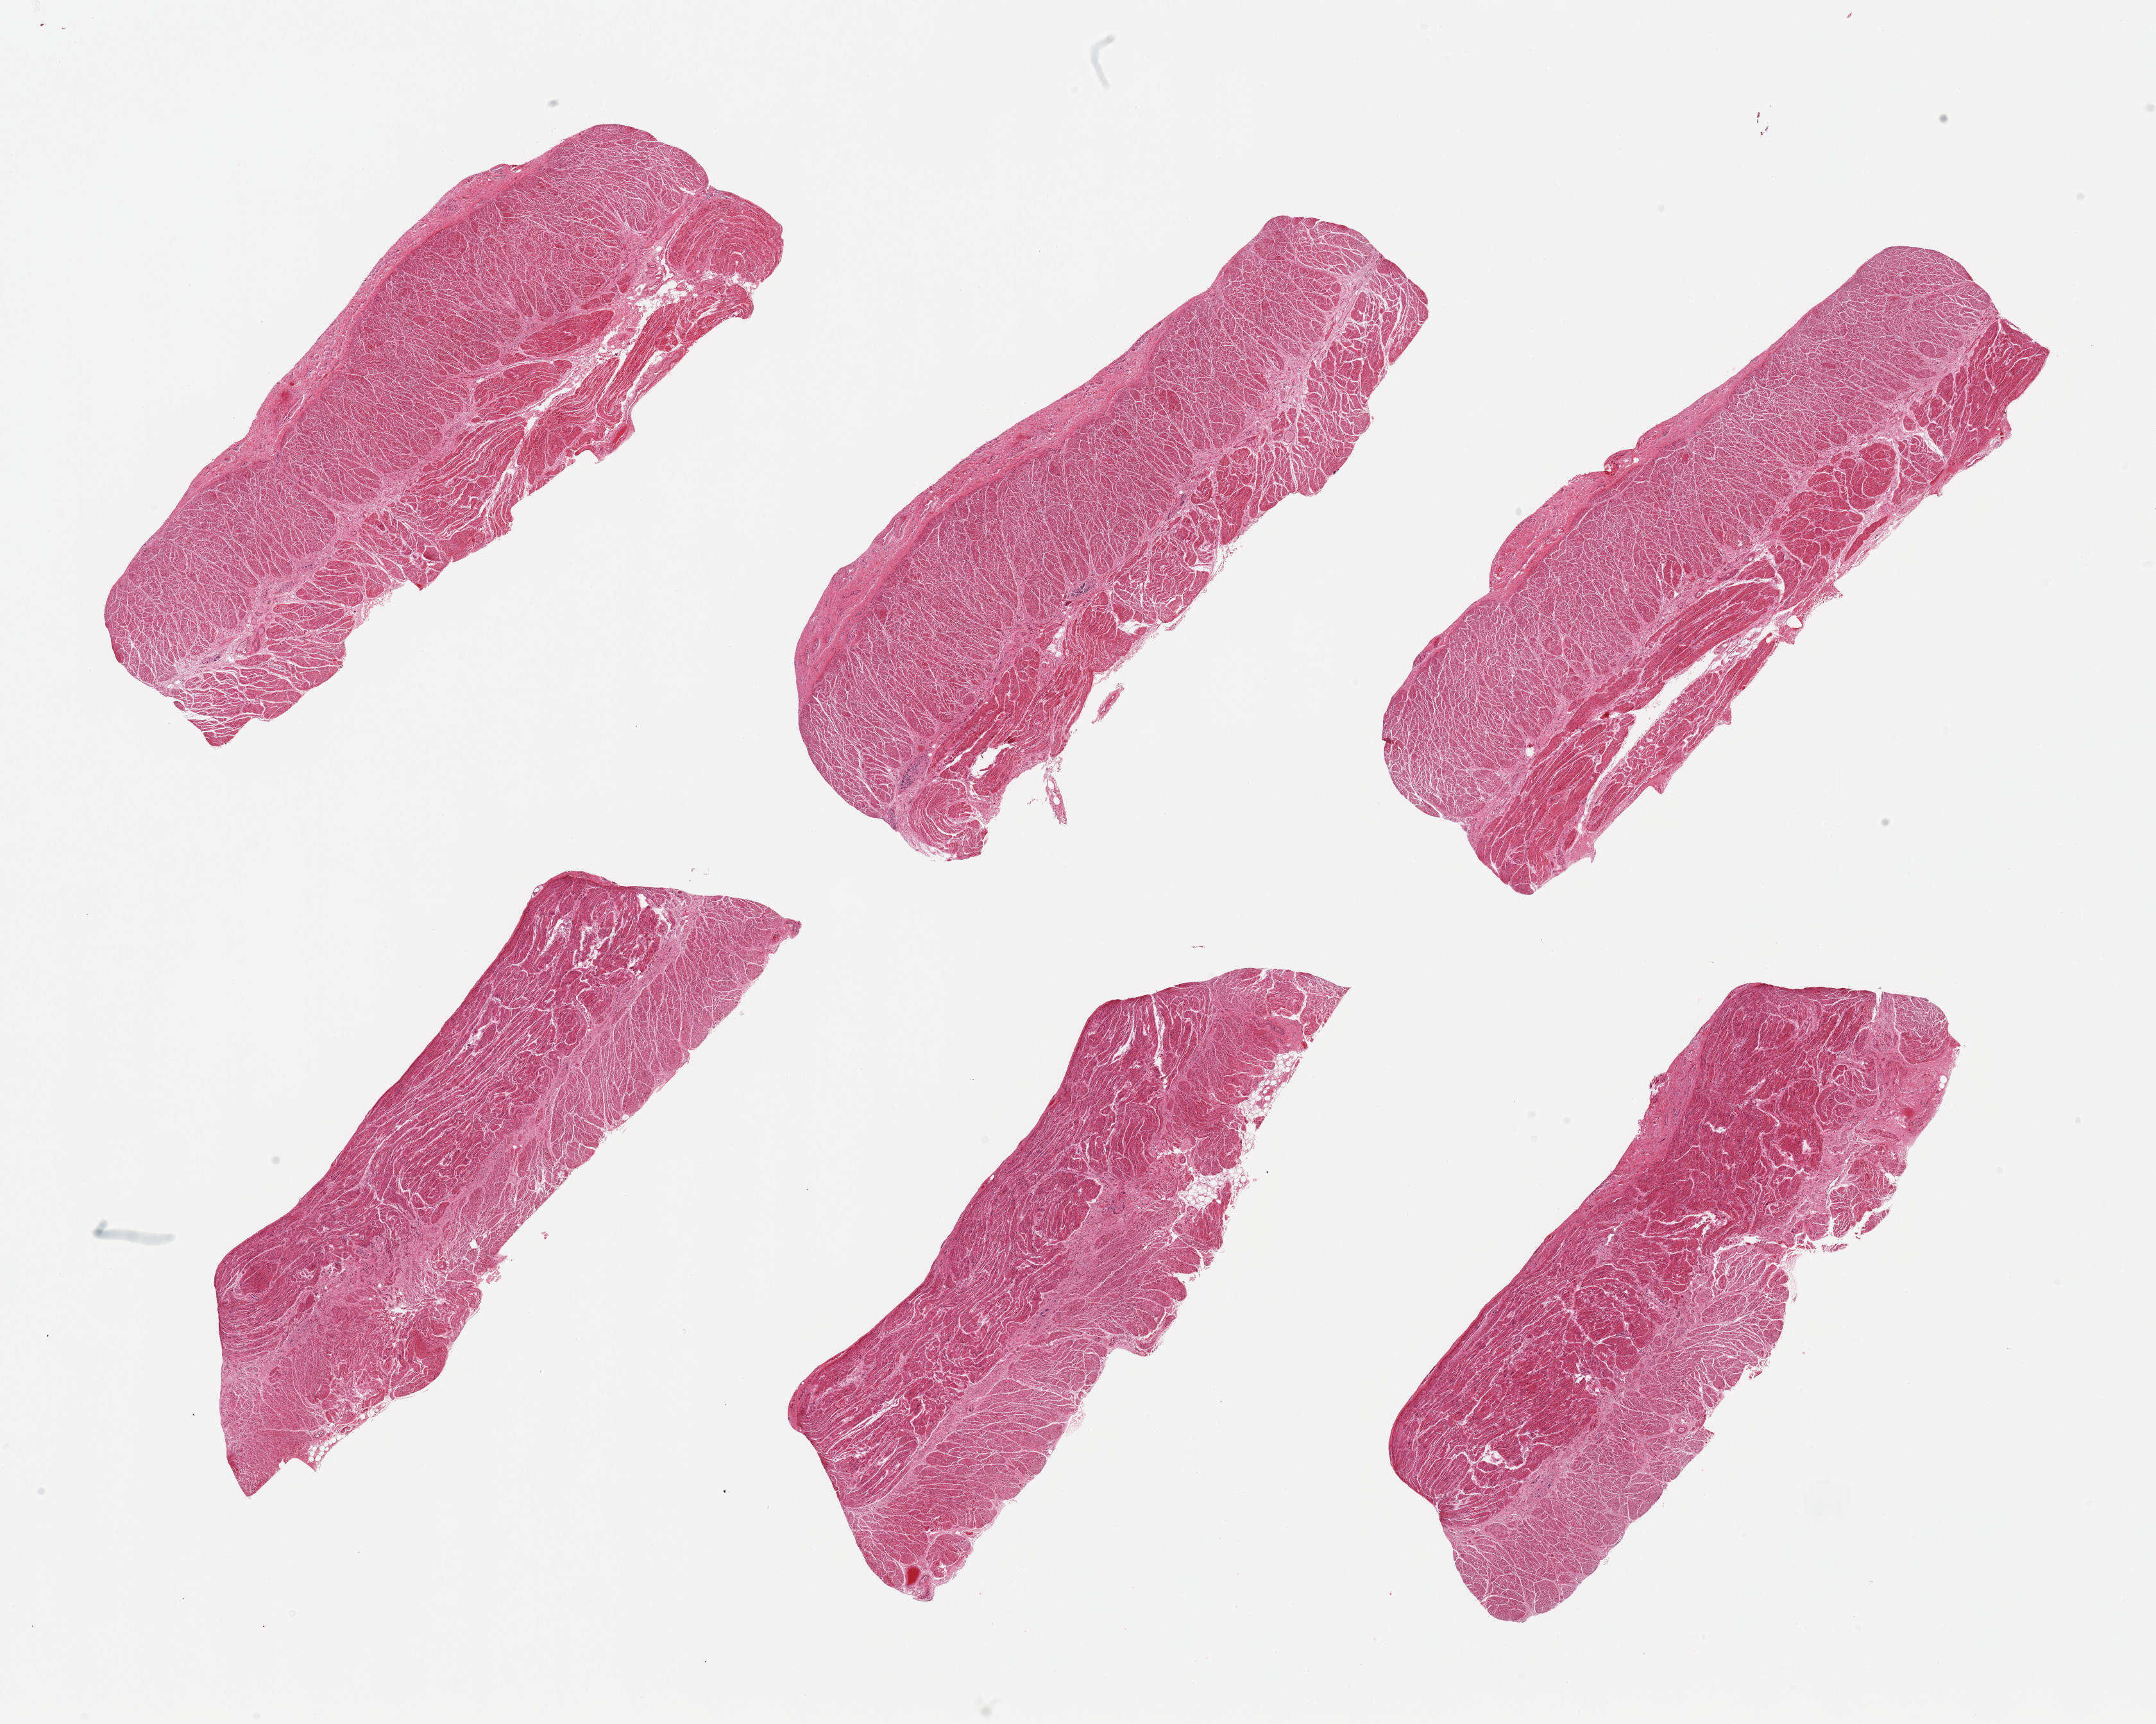
Digitized hematoxylin and eosin (H&E)-stained section, low-resolution overview of the scanned area, about 26.6 x 21.2 mm; PAXgene-fixed, paraffin-embedded tissue; sampled site (target tissue): esophageal muscle; tissue donor sample. Female donor.
• pathologist's review note for this sample: 6 pieces; well trimmed muscle